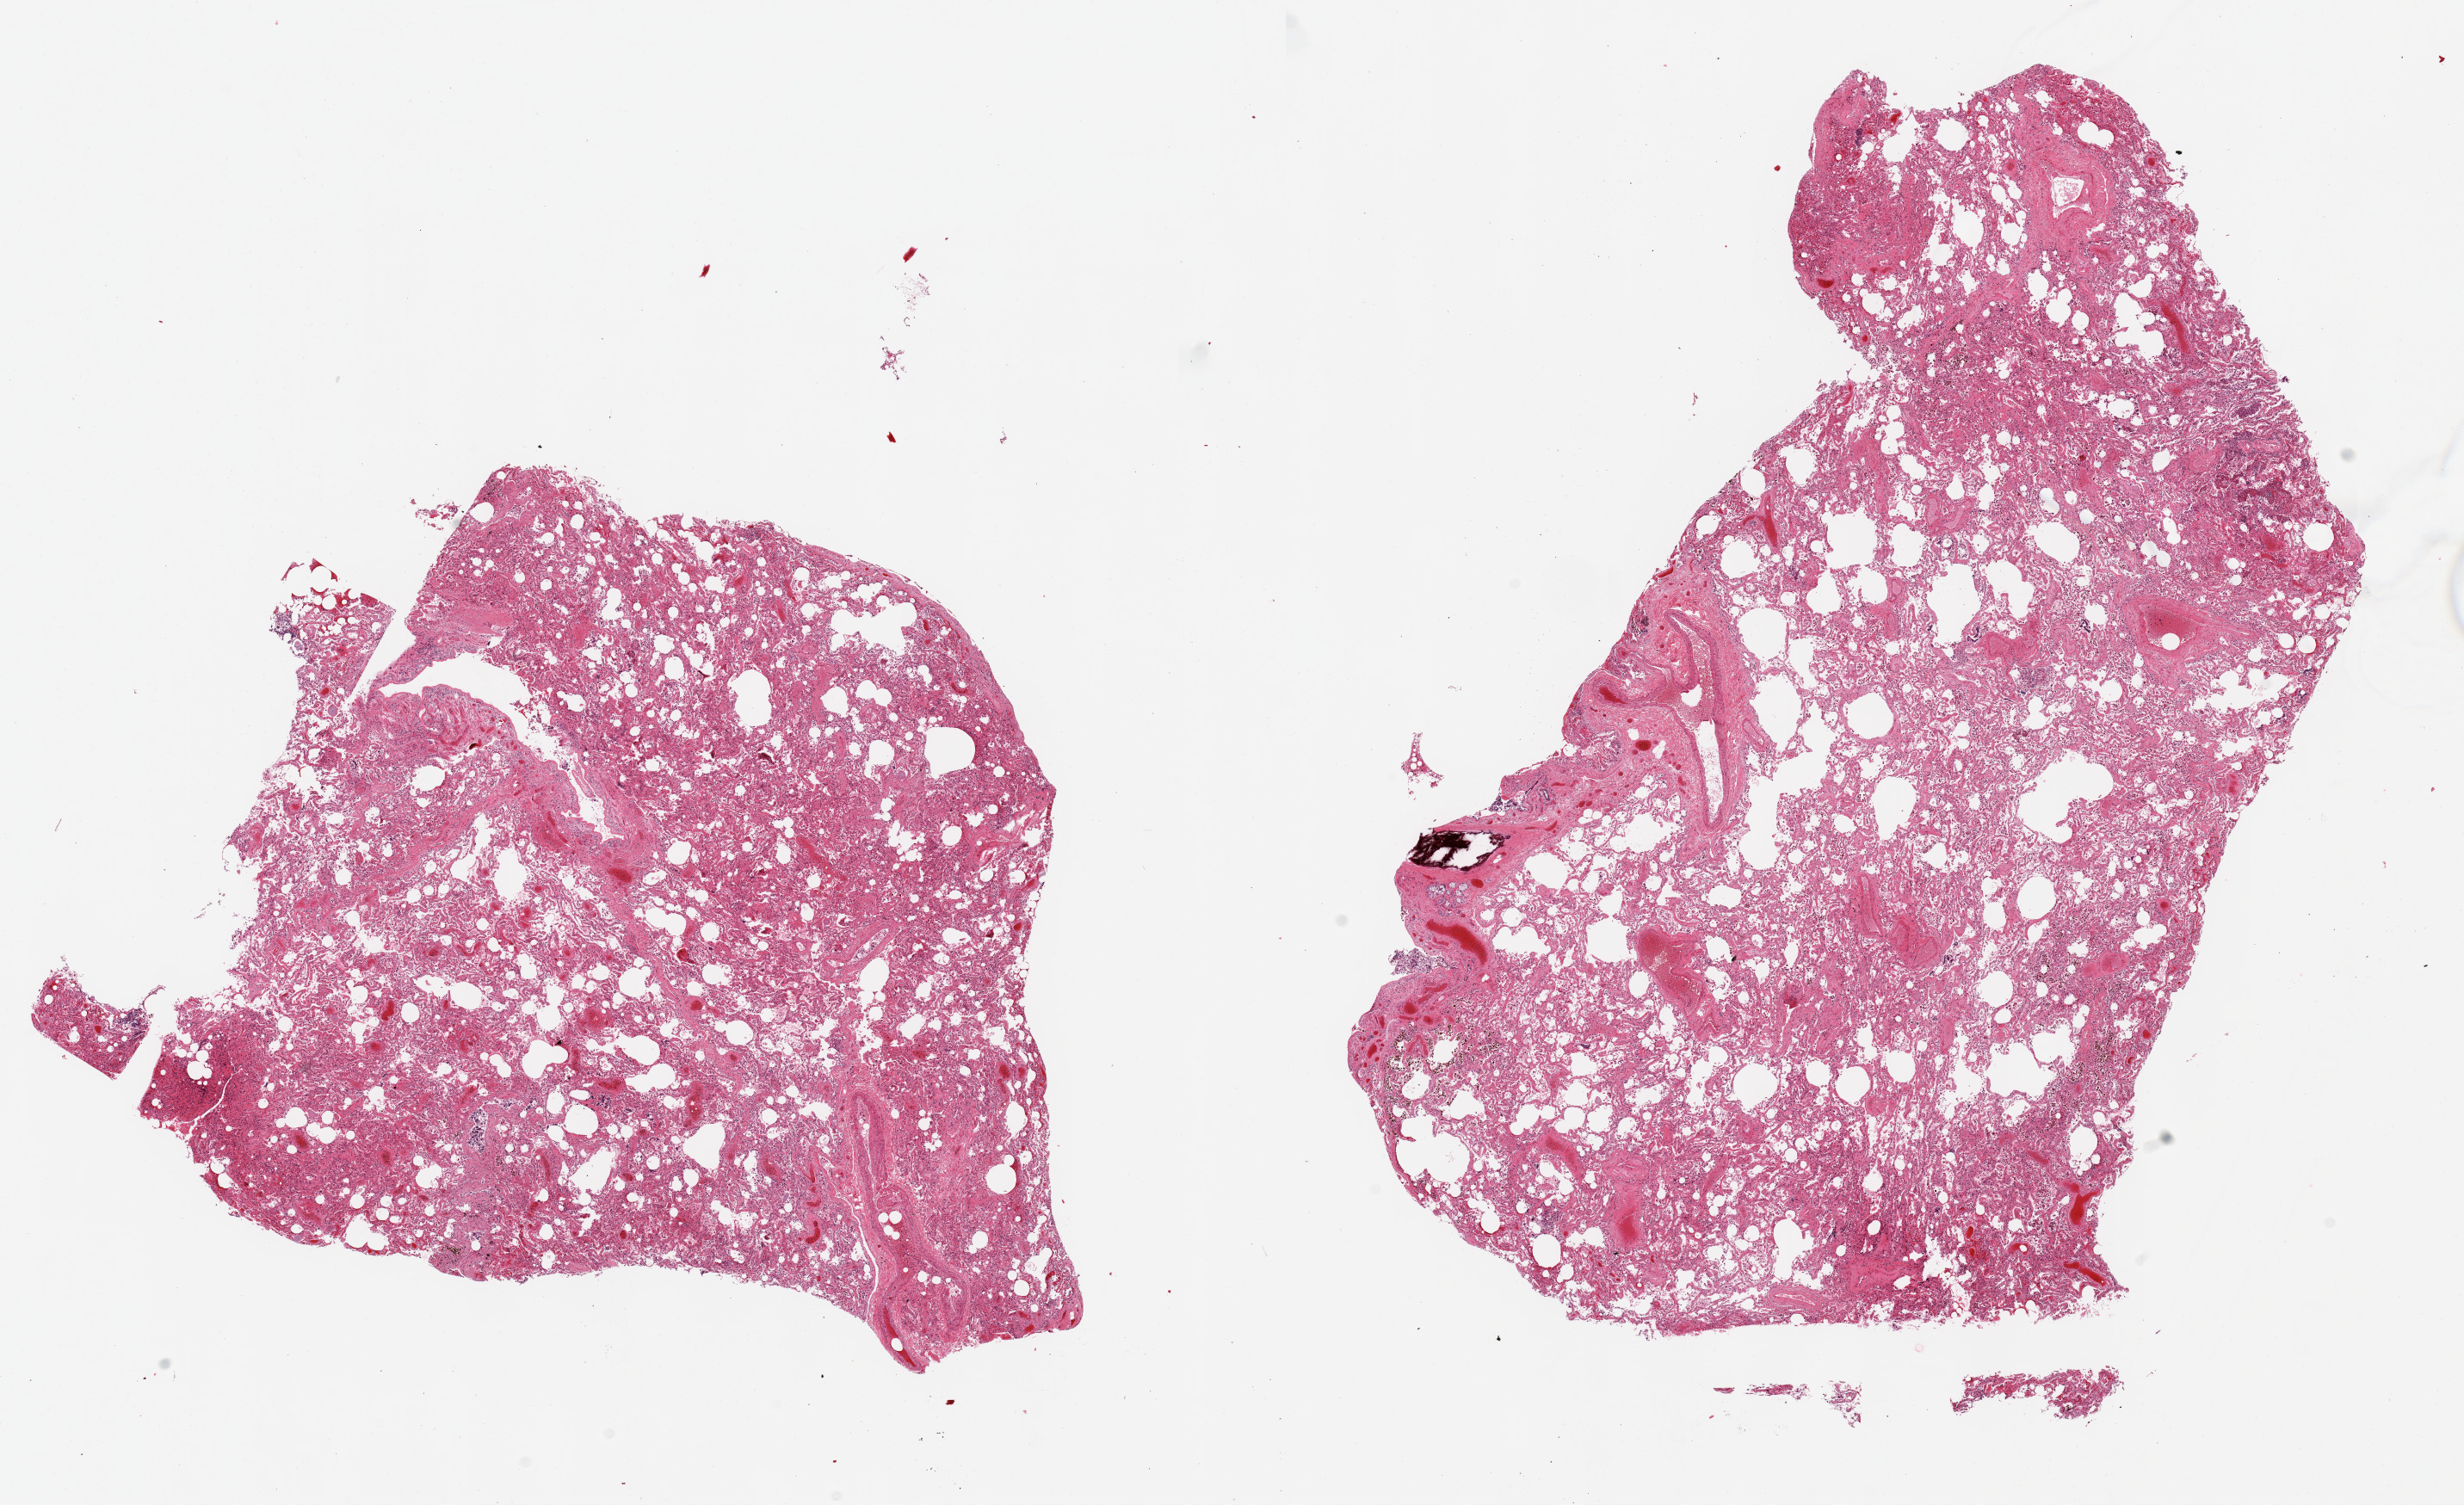
Whole-slide image, haematoxylin and eosin stain, brightfield, whole scanned area (about 22.6 x 13.8 mm, acquisition: 20x scan) shown as a low-resolution overview. PAXgene-fixed paraffin-embedded (PFPE) section. Sampled site (target tissue): lung. Tissue donor sample.
Reviewer comment on this tissue sample: 2 pieces; congestion and aggregates of hemosiderinophages.